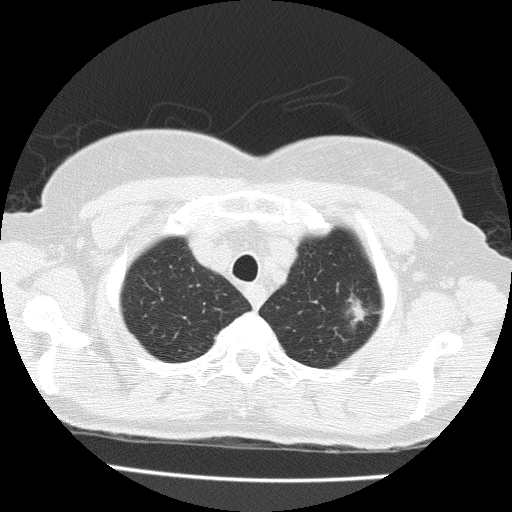
Low-dose screening chest CT, axial slice. Baseline annual screen. Lung window (W 1500 / L -600 HU). 2 mm slice thickness. Lung (sharp) reconstruction kernel (FC51). Female participant, aged 71 years at enrolment.
• Lesion marked by an expert reader, bounding box <338,291,388,336> (left, top, right, bottom; pixels).
• The exam's reader record, not a measurement of the box and not confirmed to be the same lesion: non-calcified nodule or mass ≥4 mm, left upper lobe, 15 × 10 mm, spiculated (stellate) margins, soft tissue attenuation.
• Lung cancer was diagnosed 49 days after this screen: adenocarcinoma with mixed subtypes, left upper lobe, well differentiated (G1), stage IA (AJCC 6th edition), 15 mm at pathology.